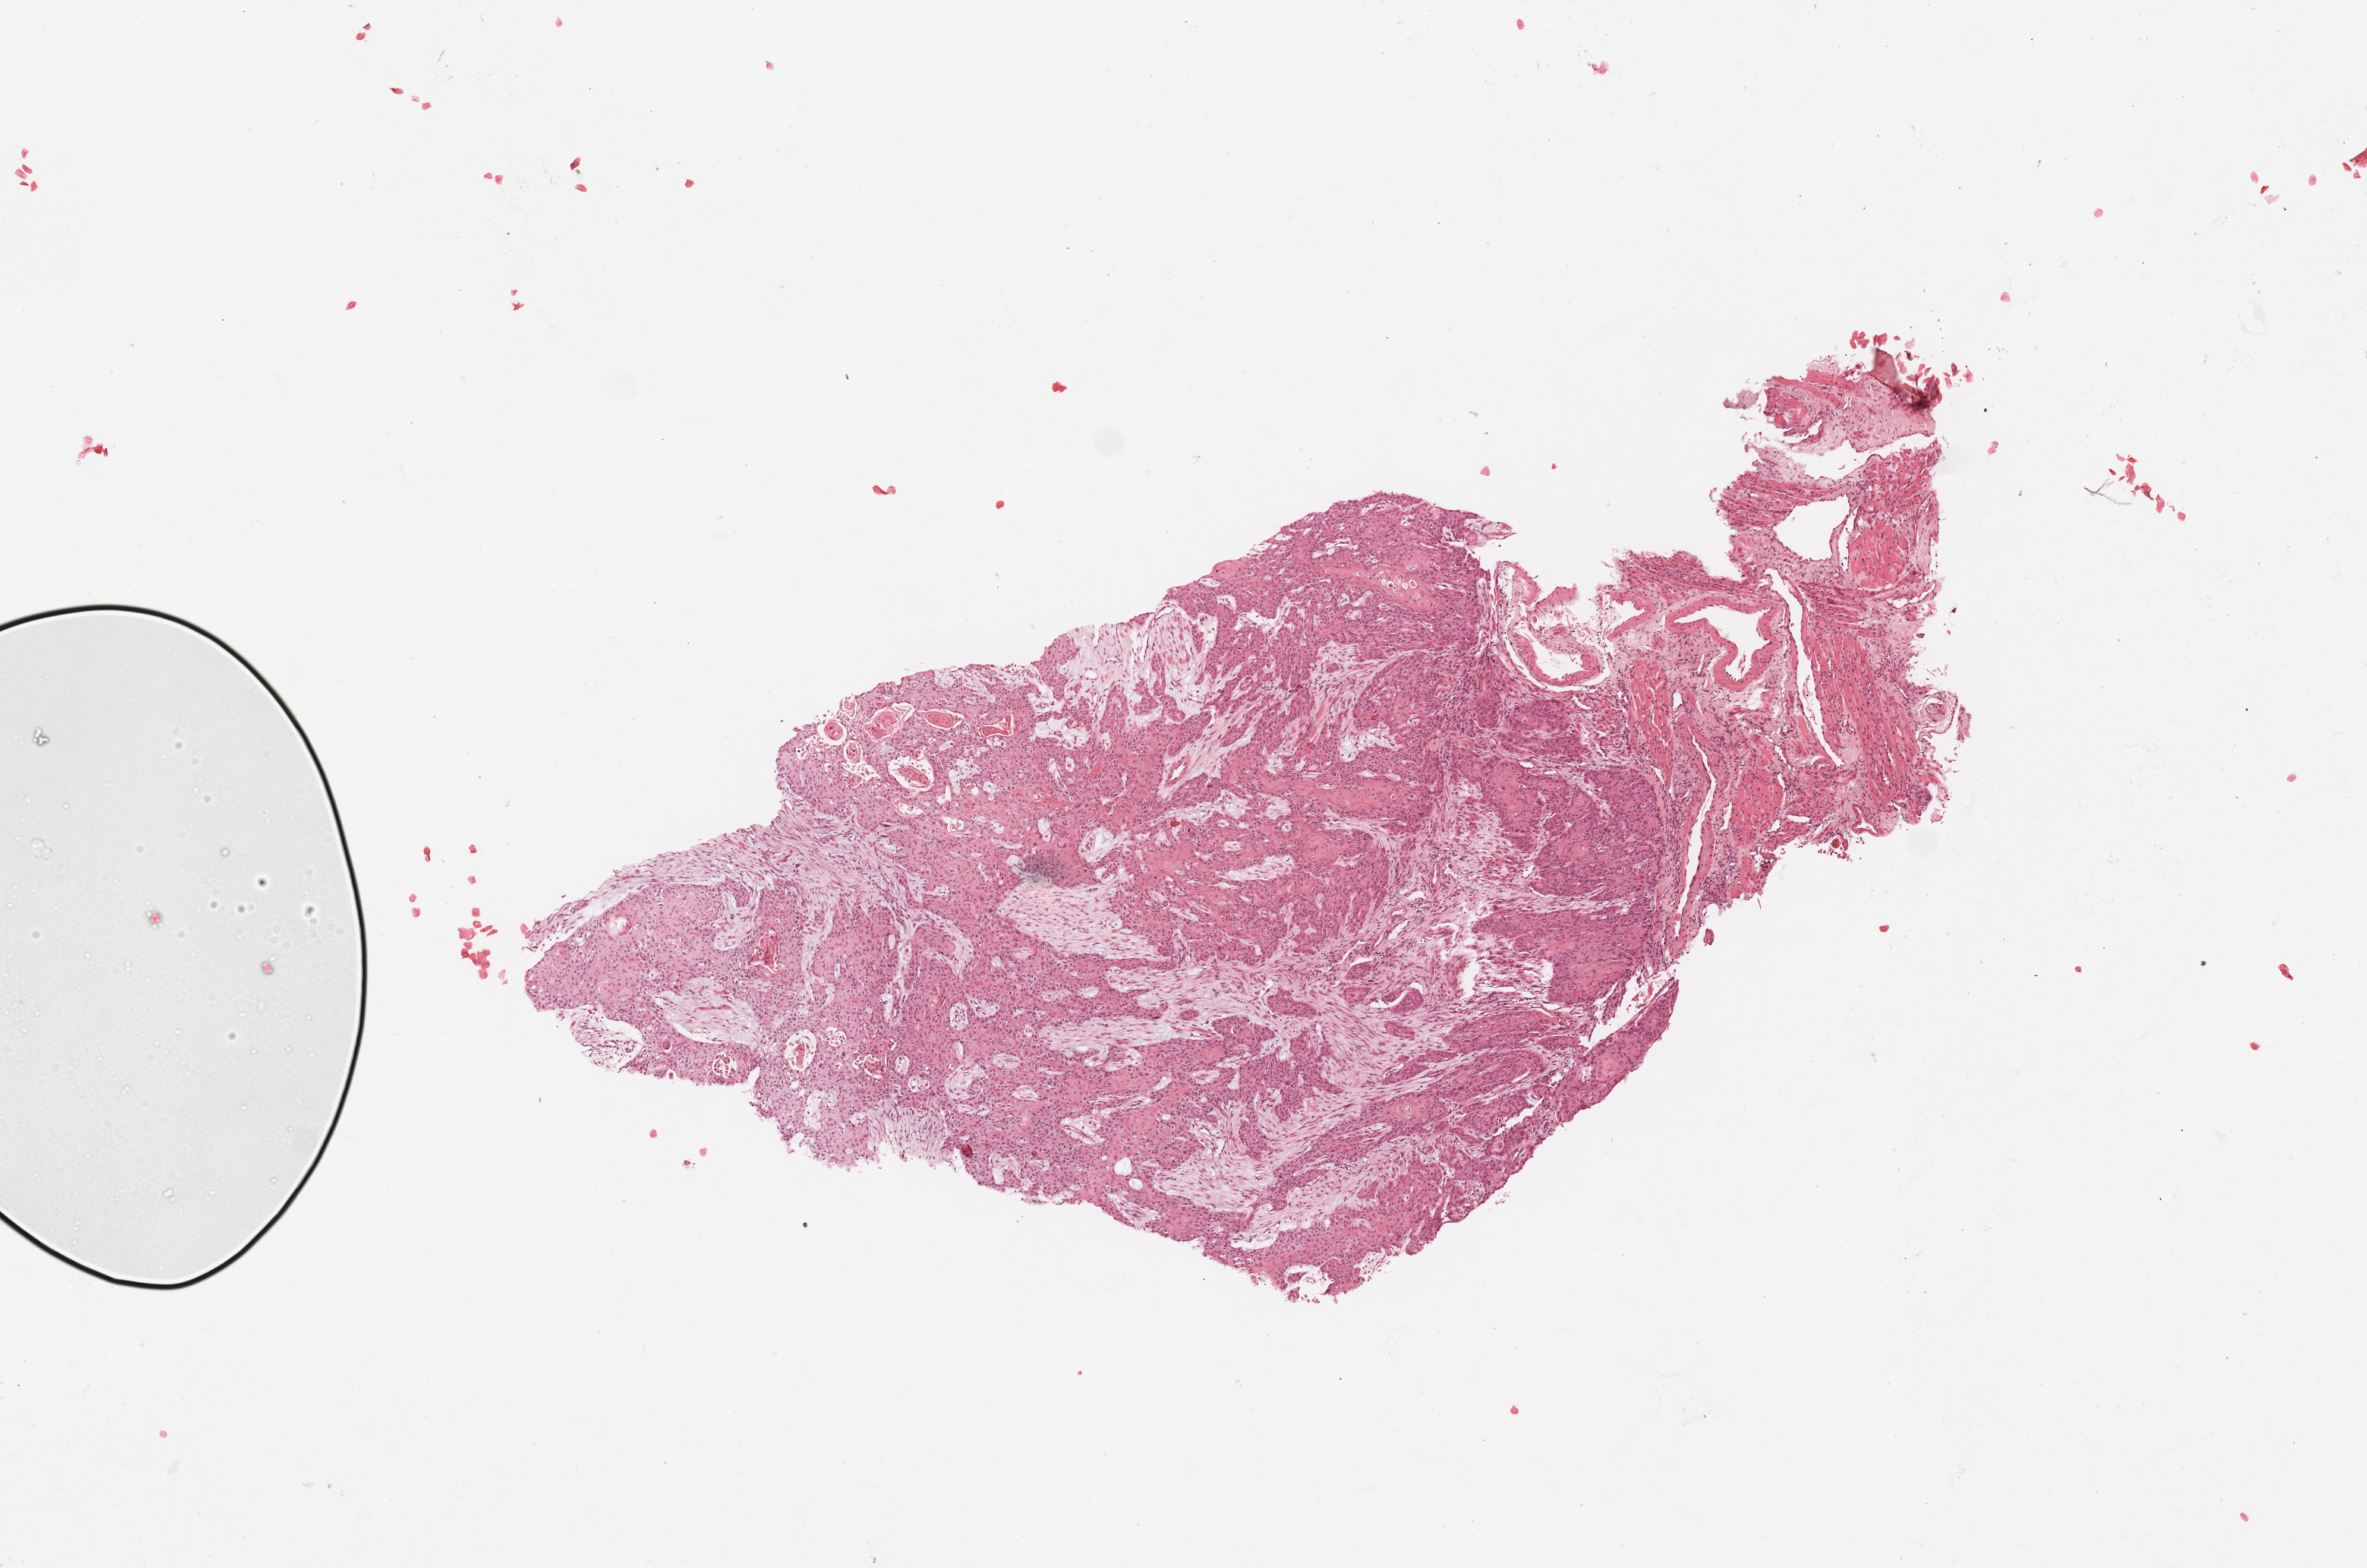
Whole-slide histology image, H&E, whole scanned area (about 7.9 x 5.2 mm, acquisition: 20x scan) shown as a low-resolution overview; tumour tissue sample, sampled site: oral cavity. Patient: male, age 58 years. Histologic grade: G2 (moderately differentiated). Slide review estimates, as recorded: tumour nuclei 80%, necrosis 5%.
• AJCC pathologic stage: IVA
• histologic diagnosis: Squamous cell carcinoma, NOS (overlapping lesion of lip, oral cavity and pharynx)